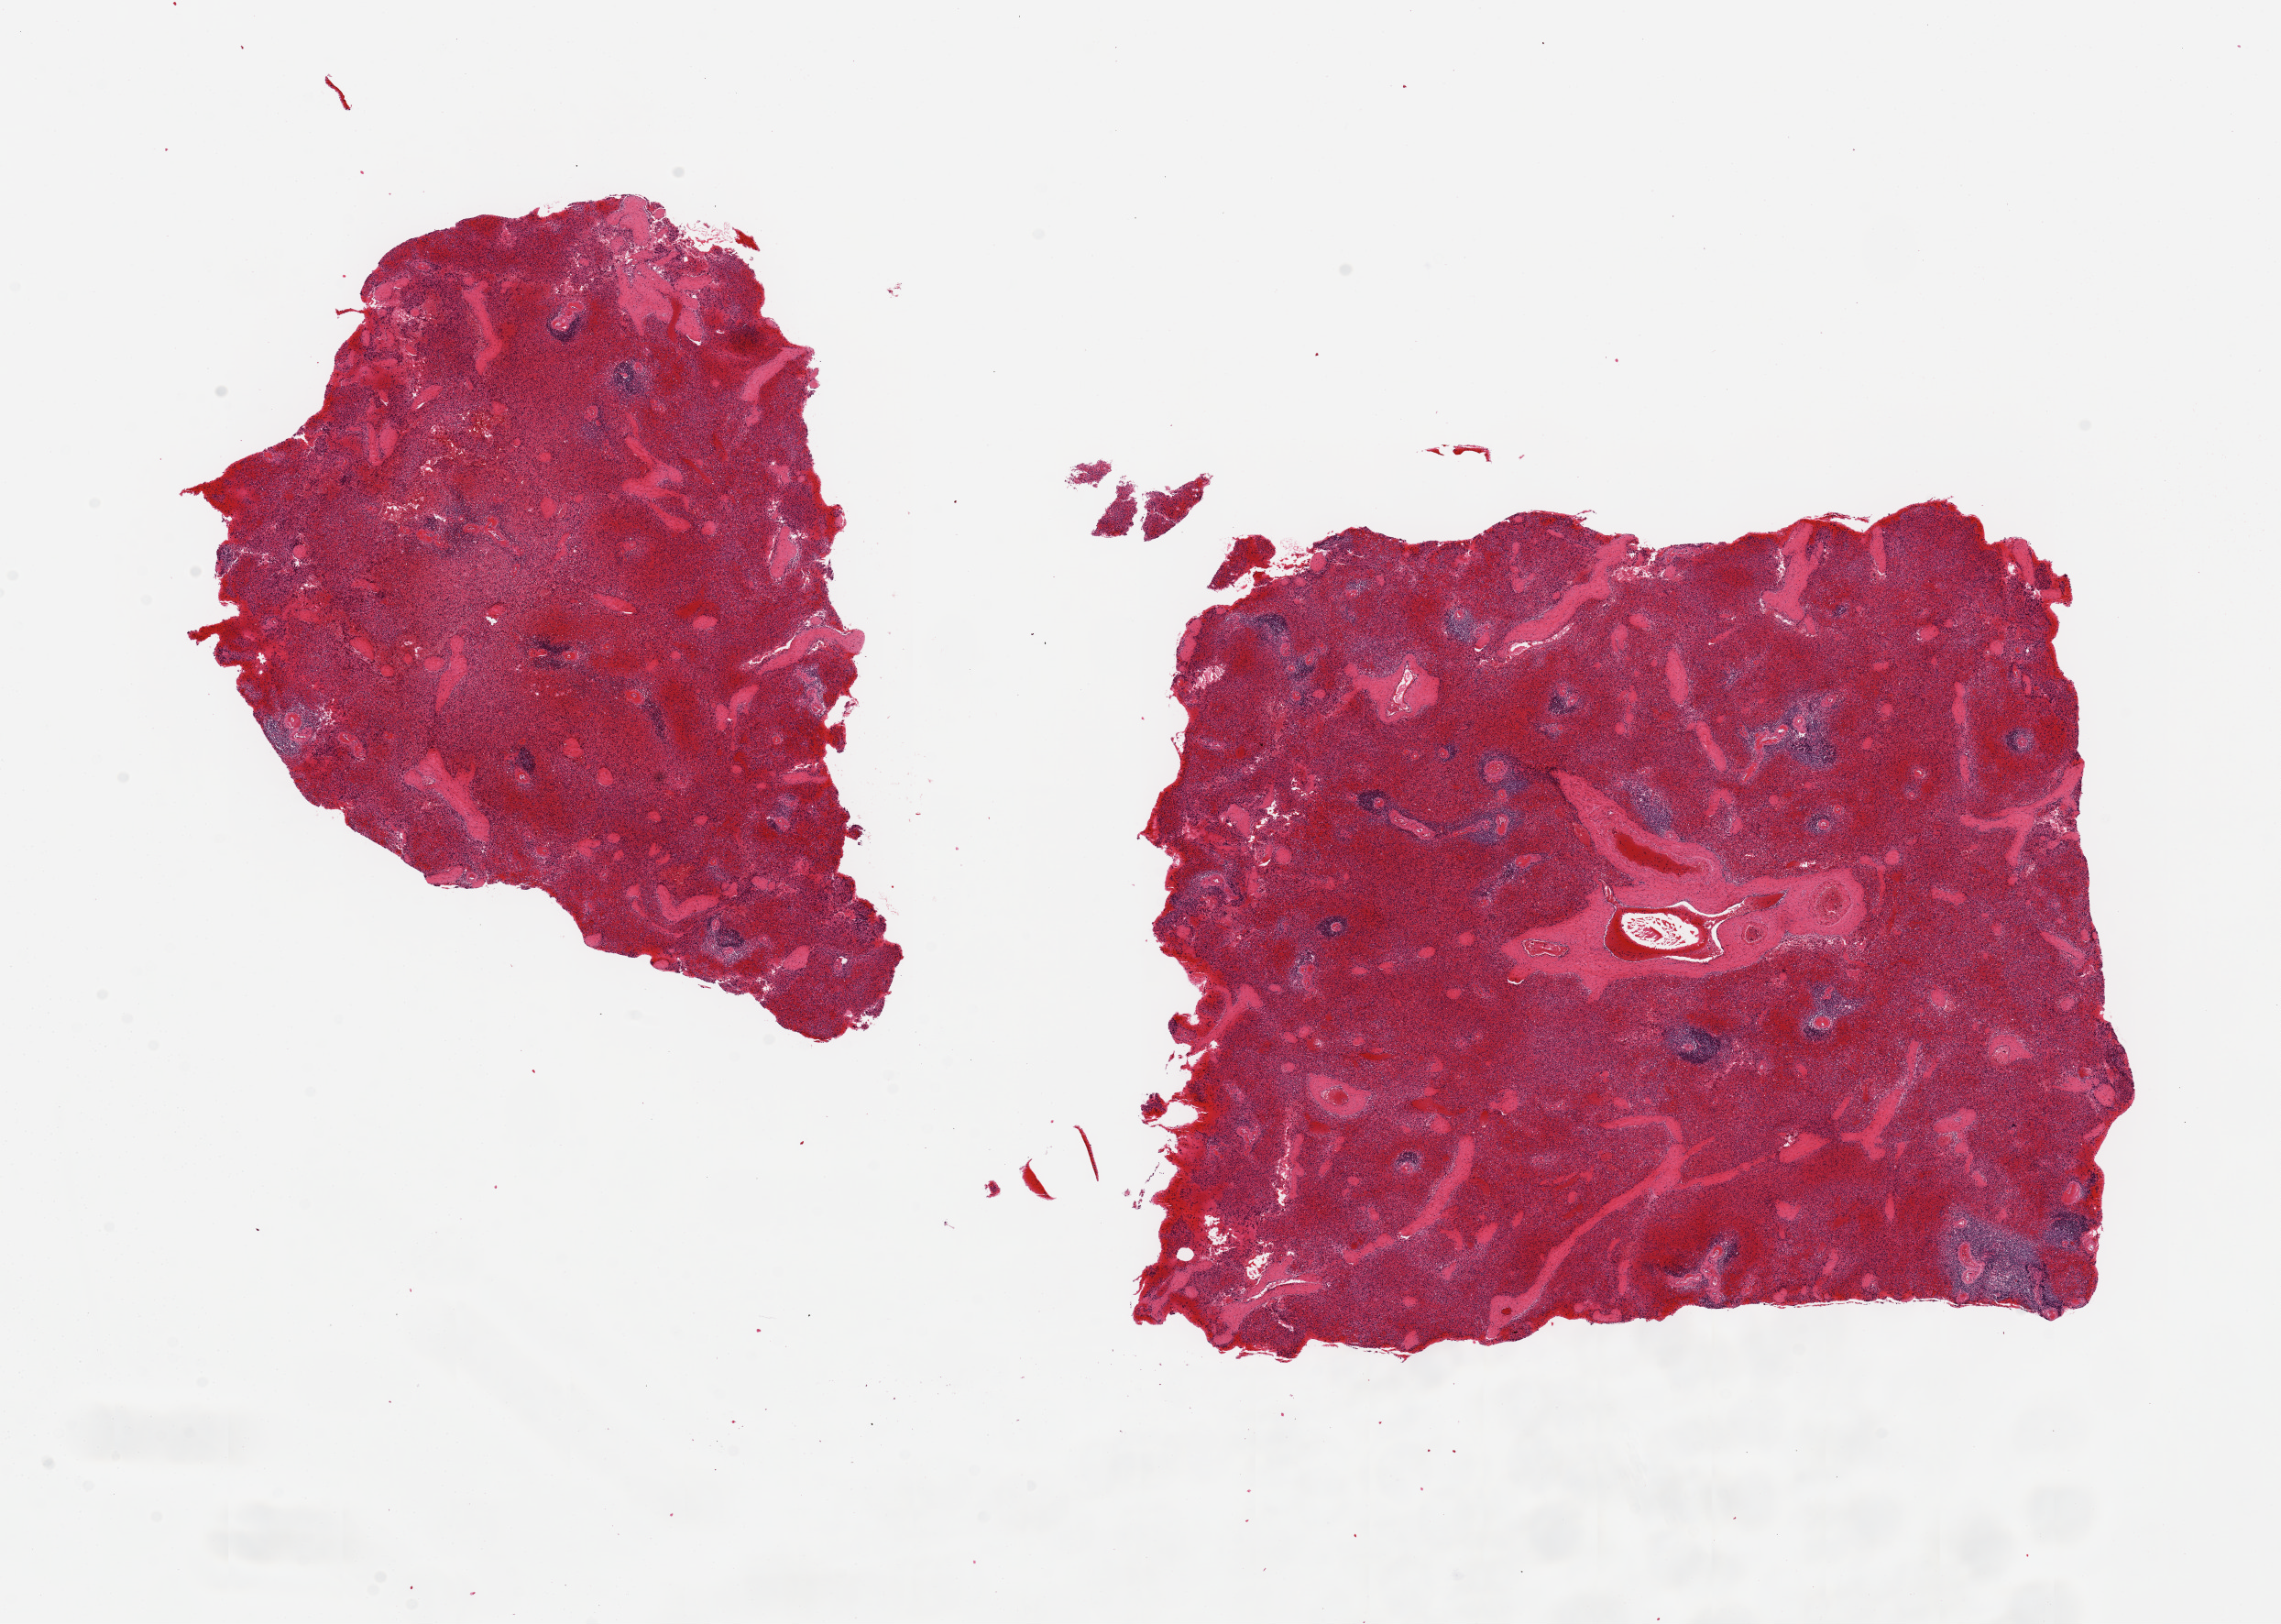
Whole-slide image, haematoxylin and eosin stain, low-resolution overview of the scanned area, about 19.7 x 14.0 mm (slide scanned at 20x); PAXgene-fixed, paraffin-embedded tissue; sampled site (target tissue): spleen; donor tissue sample. Donor: male.
Reviewer comment on this tissue sample: 2 pieces 8x7 & 7x5 mm; heavily congested.